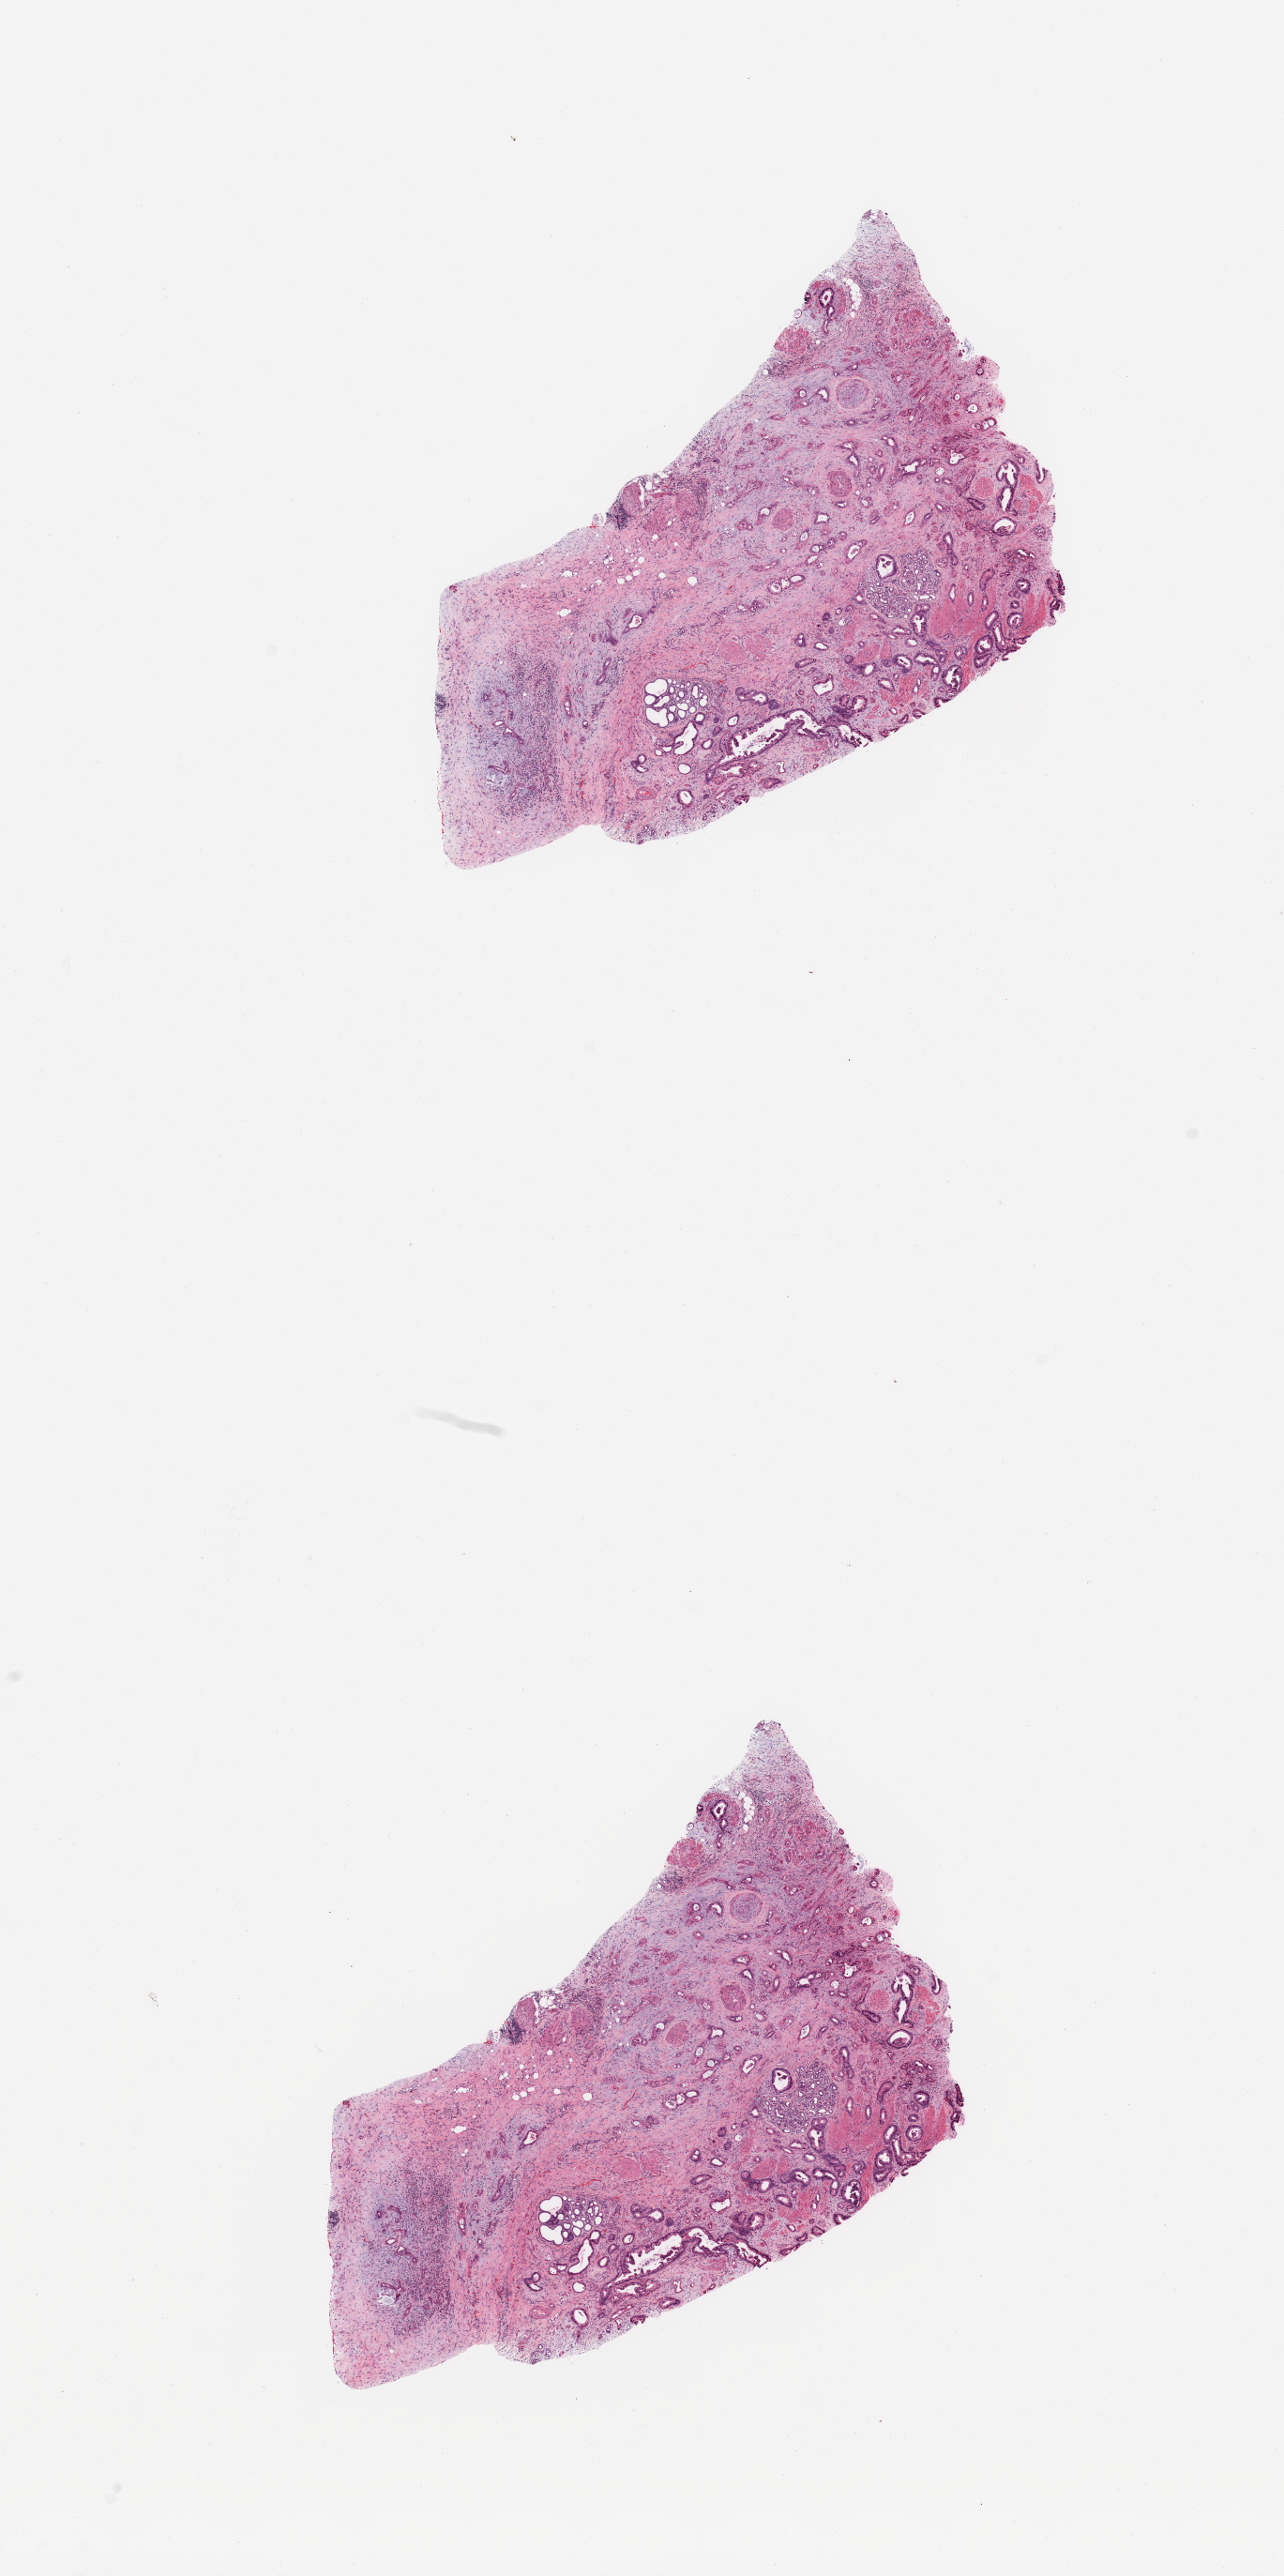
Whole-slide histology image, Hematoxylin and eosin (H&E) stained — whole scanned area (about 10.8 x 21.7 mm, from a 20x scan) shown as a low-resolution overview, tumour tissue sample, sampled site: pancreas. Male, 80 y/o. Histologic grade: G2 (moderately differentiated). Composition of this section per pathologist review: tumour nuclei 50%, necrosis 0%.
AJCC pathologic stage: IIB. Primary tumour site (as recorded): head. Histologic diagnosis: Infiltrating duct carcinoma, NOS.